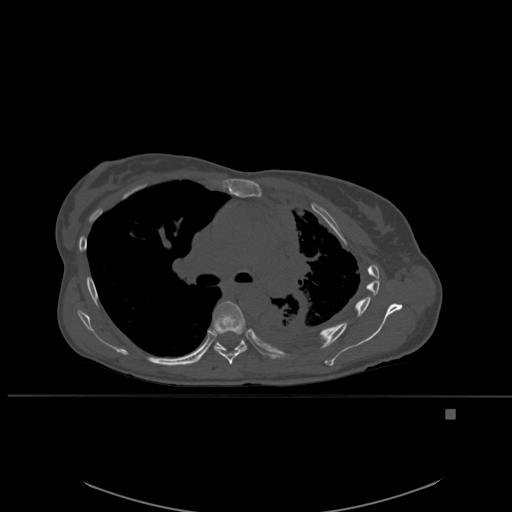
CT including the spine, one axial slice. Slice 377 of 537 in the series (ordered by position). Bone window (W 1800 / L 400 HU). 512 × 512 image matrix, field of view 440 × 440 mm. Patient: female, 45 years. Case-level facts recorded for this patient, not image findings: primary cancer: lung.
Annotated regions visible in this slice (semi-automatic segmentation, software-assisted and operator-edited):
- T6 vertebra: box from (x=212, y=301) to (x=248, y=365) px
- T7 vertebra: (x=196, y=338)–(x=247, y=362)